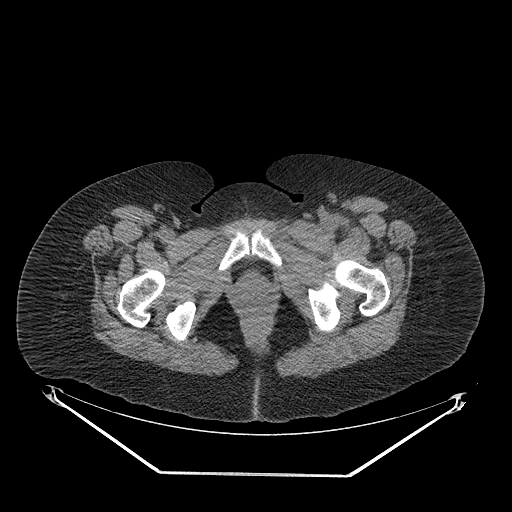
CT of an extremity soft-tissue mass (from a PET/CT study), one axial slice; position 52 of 267 along the scan axis; 140 kVp; soft-tissue window (W 400 / L 40 HU); 3.75 mm slice thickness; 512 × 512 image matrix. Female patient. Case-level facts recorded for this patient, not image findings: histological type: myxofibrosarcoma; grade: intermediate; site of the primary tumour: left thigh.
Annotated regions visible in this slice (expert contour drawn on MRI and transferred to this co-registered scan by the dataset authors):
- gross tumour volume including surrounding oedema: bounding box (x1, y1, x2, y2) in pixels: (269, 218, 357, 252)